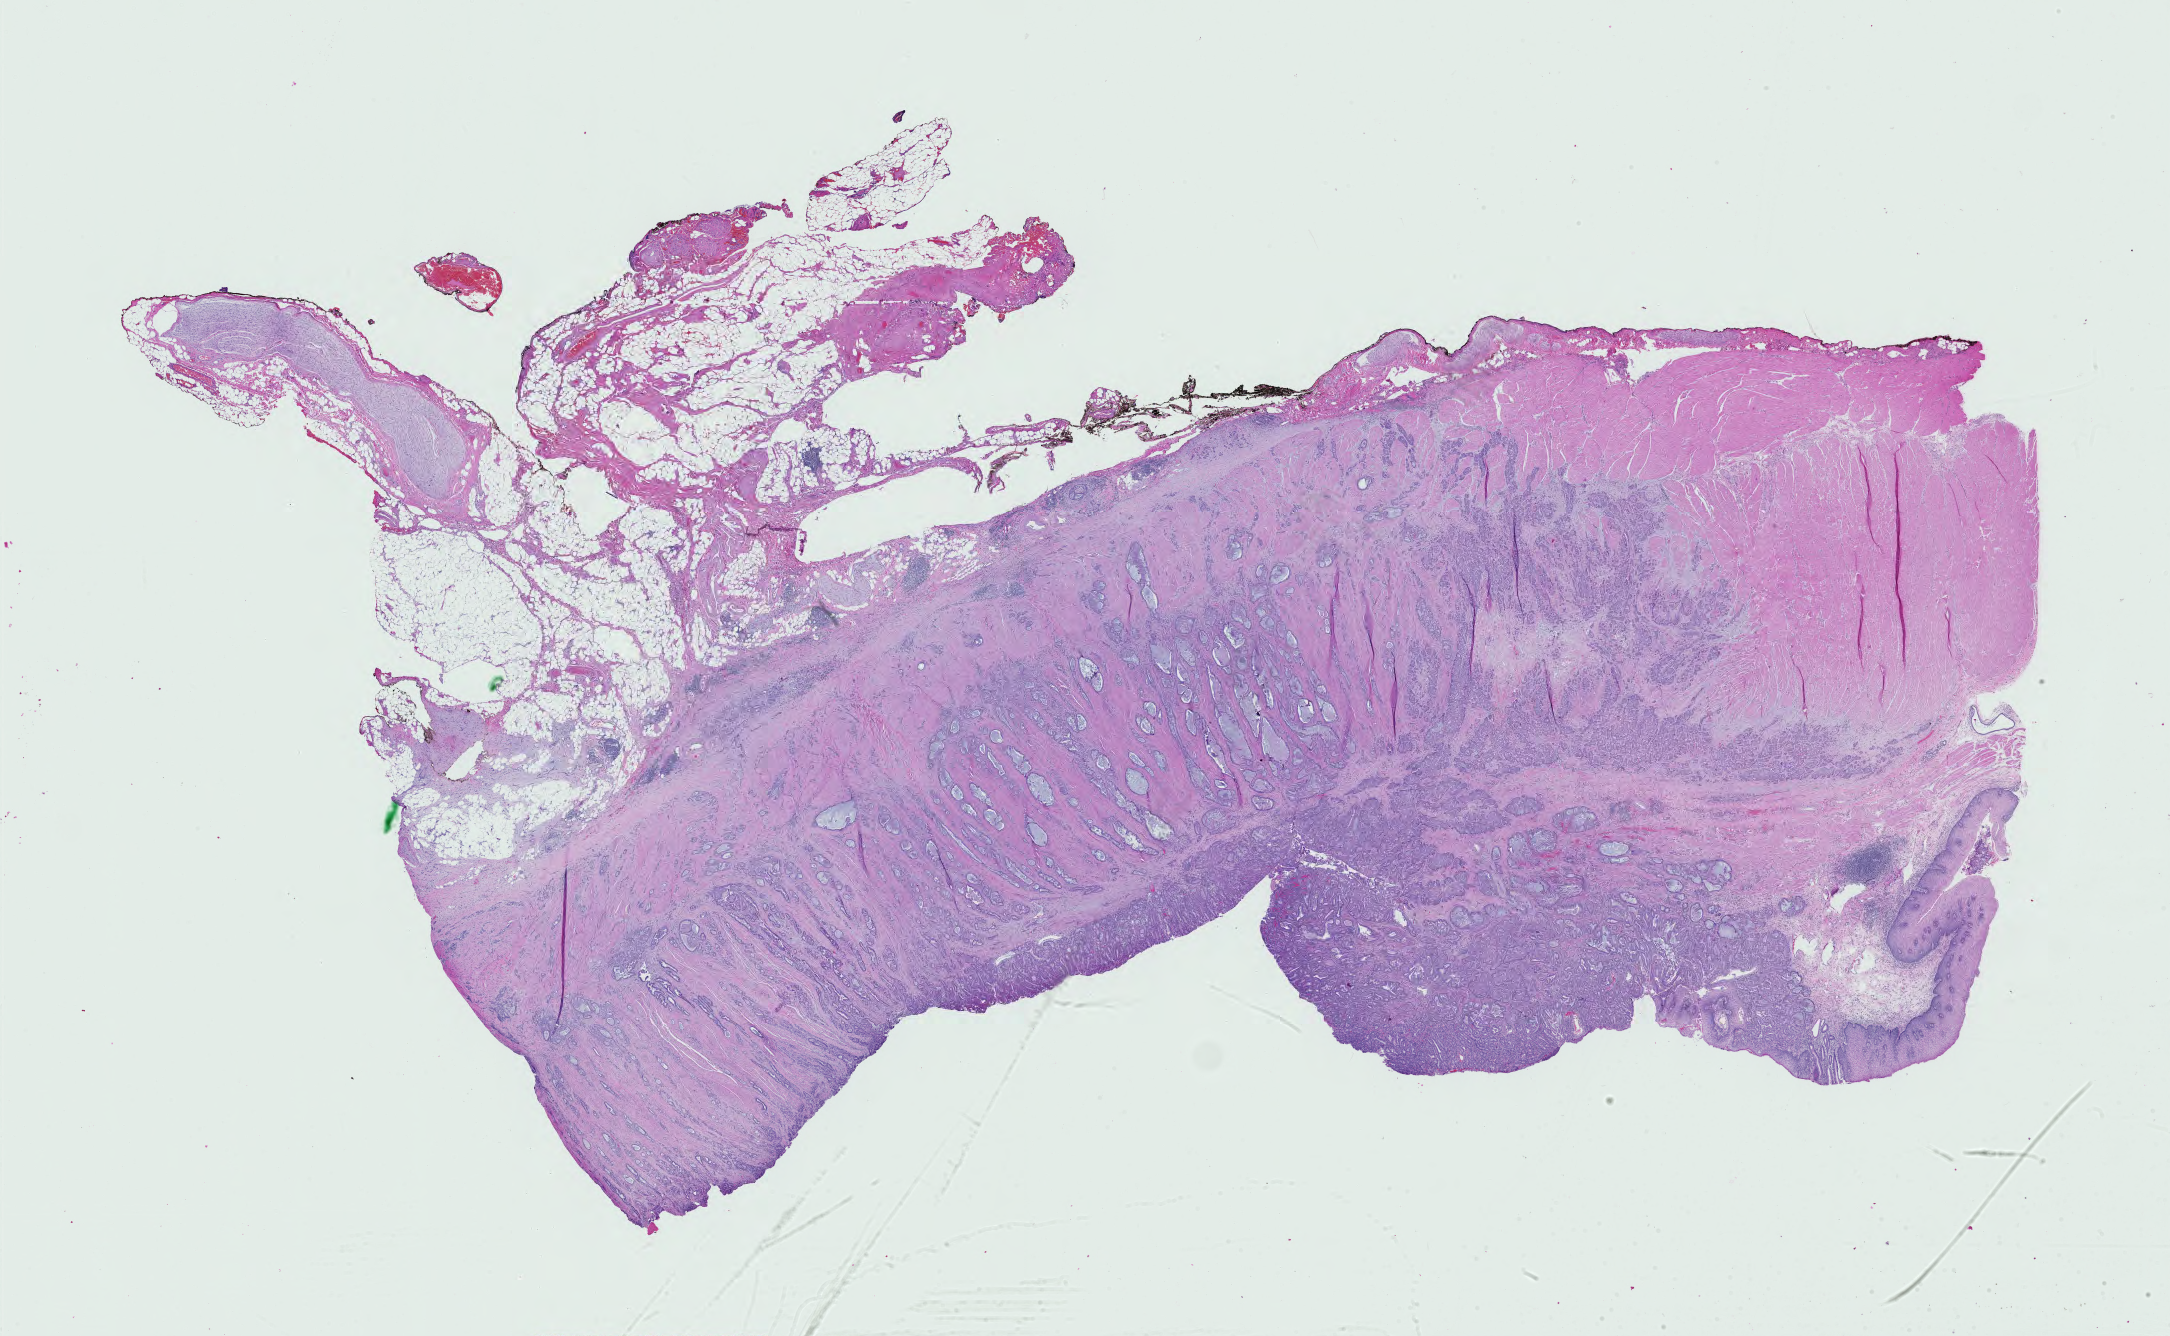
Hematoxylin and eosin (H&E) stained whole-slide image, low-resolution overview of the scanned area, about 31.5 x 19.4 mm. FFPE section. Primary tumour sample from the esophagus. Patient: male, age at initial diagnosis 61 years. Histologic grade: G2 (moderately differentiated).
• AJCC pathologic stage: IIIB (7th edition)
• lymph nodes positive (case pathology): 3 of 62 examined
• histologic diagnosis: Adenocarcinoma, NOS (lower third of esophagus)